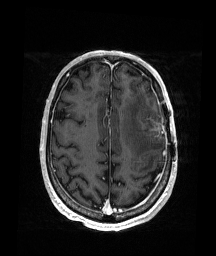
Brain MRI from a brain-tumour surgery series, one axial slice. Position 60 of 176 along the scan axis. T1-weighted post-contrast. 216 × 256 image matrix, field of view 219 × 260 mm. From the clinical record (not read from this slice): histopathology: Glioblastoma; WHO grade: 4; IDH mutation: no.
Structures marked on this image (outlined manually by an expert reader):
- tumour: bounding box [x1, y1, x2, y2] px = [141, 118, 163, 136]